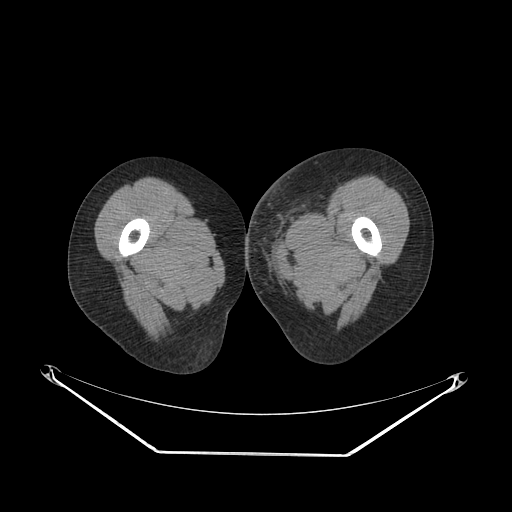
CT of an extremity soft-tissue mass (from a PET/CT study), one axial slice. Soft-tissue window (W 400 / L 40 HU). 3.75 mm slice thickness. 512 × 512 image matrix. Female patient. From the clinical record (not read from this slice): histological type: leiomyosarcoma; grade: high; site of the primary tumour: groin.
Outlined on this slice (expert contour drawn on MRI and transferred to this co-registered scan by the dataset authors):
- gross tumour volume including surrounding oedema: box from (x=246, y=189) to (x=328, y=257) px